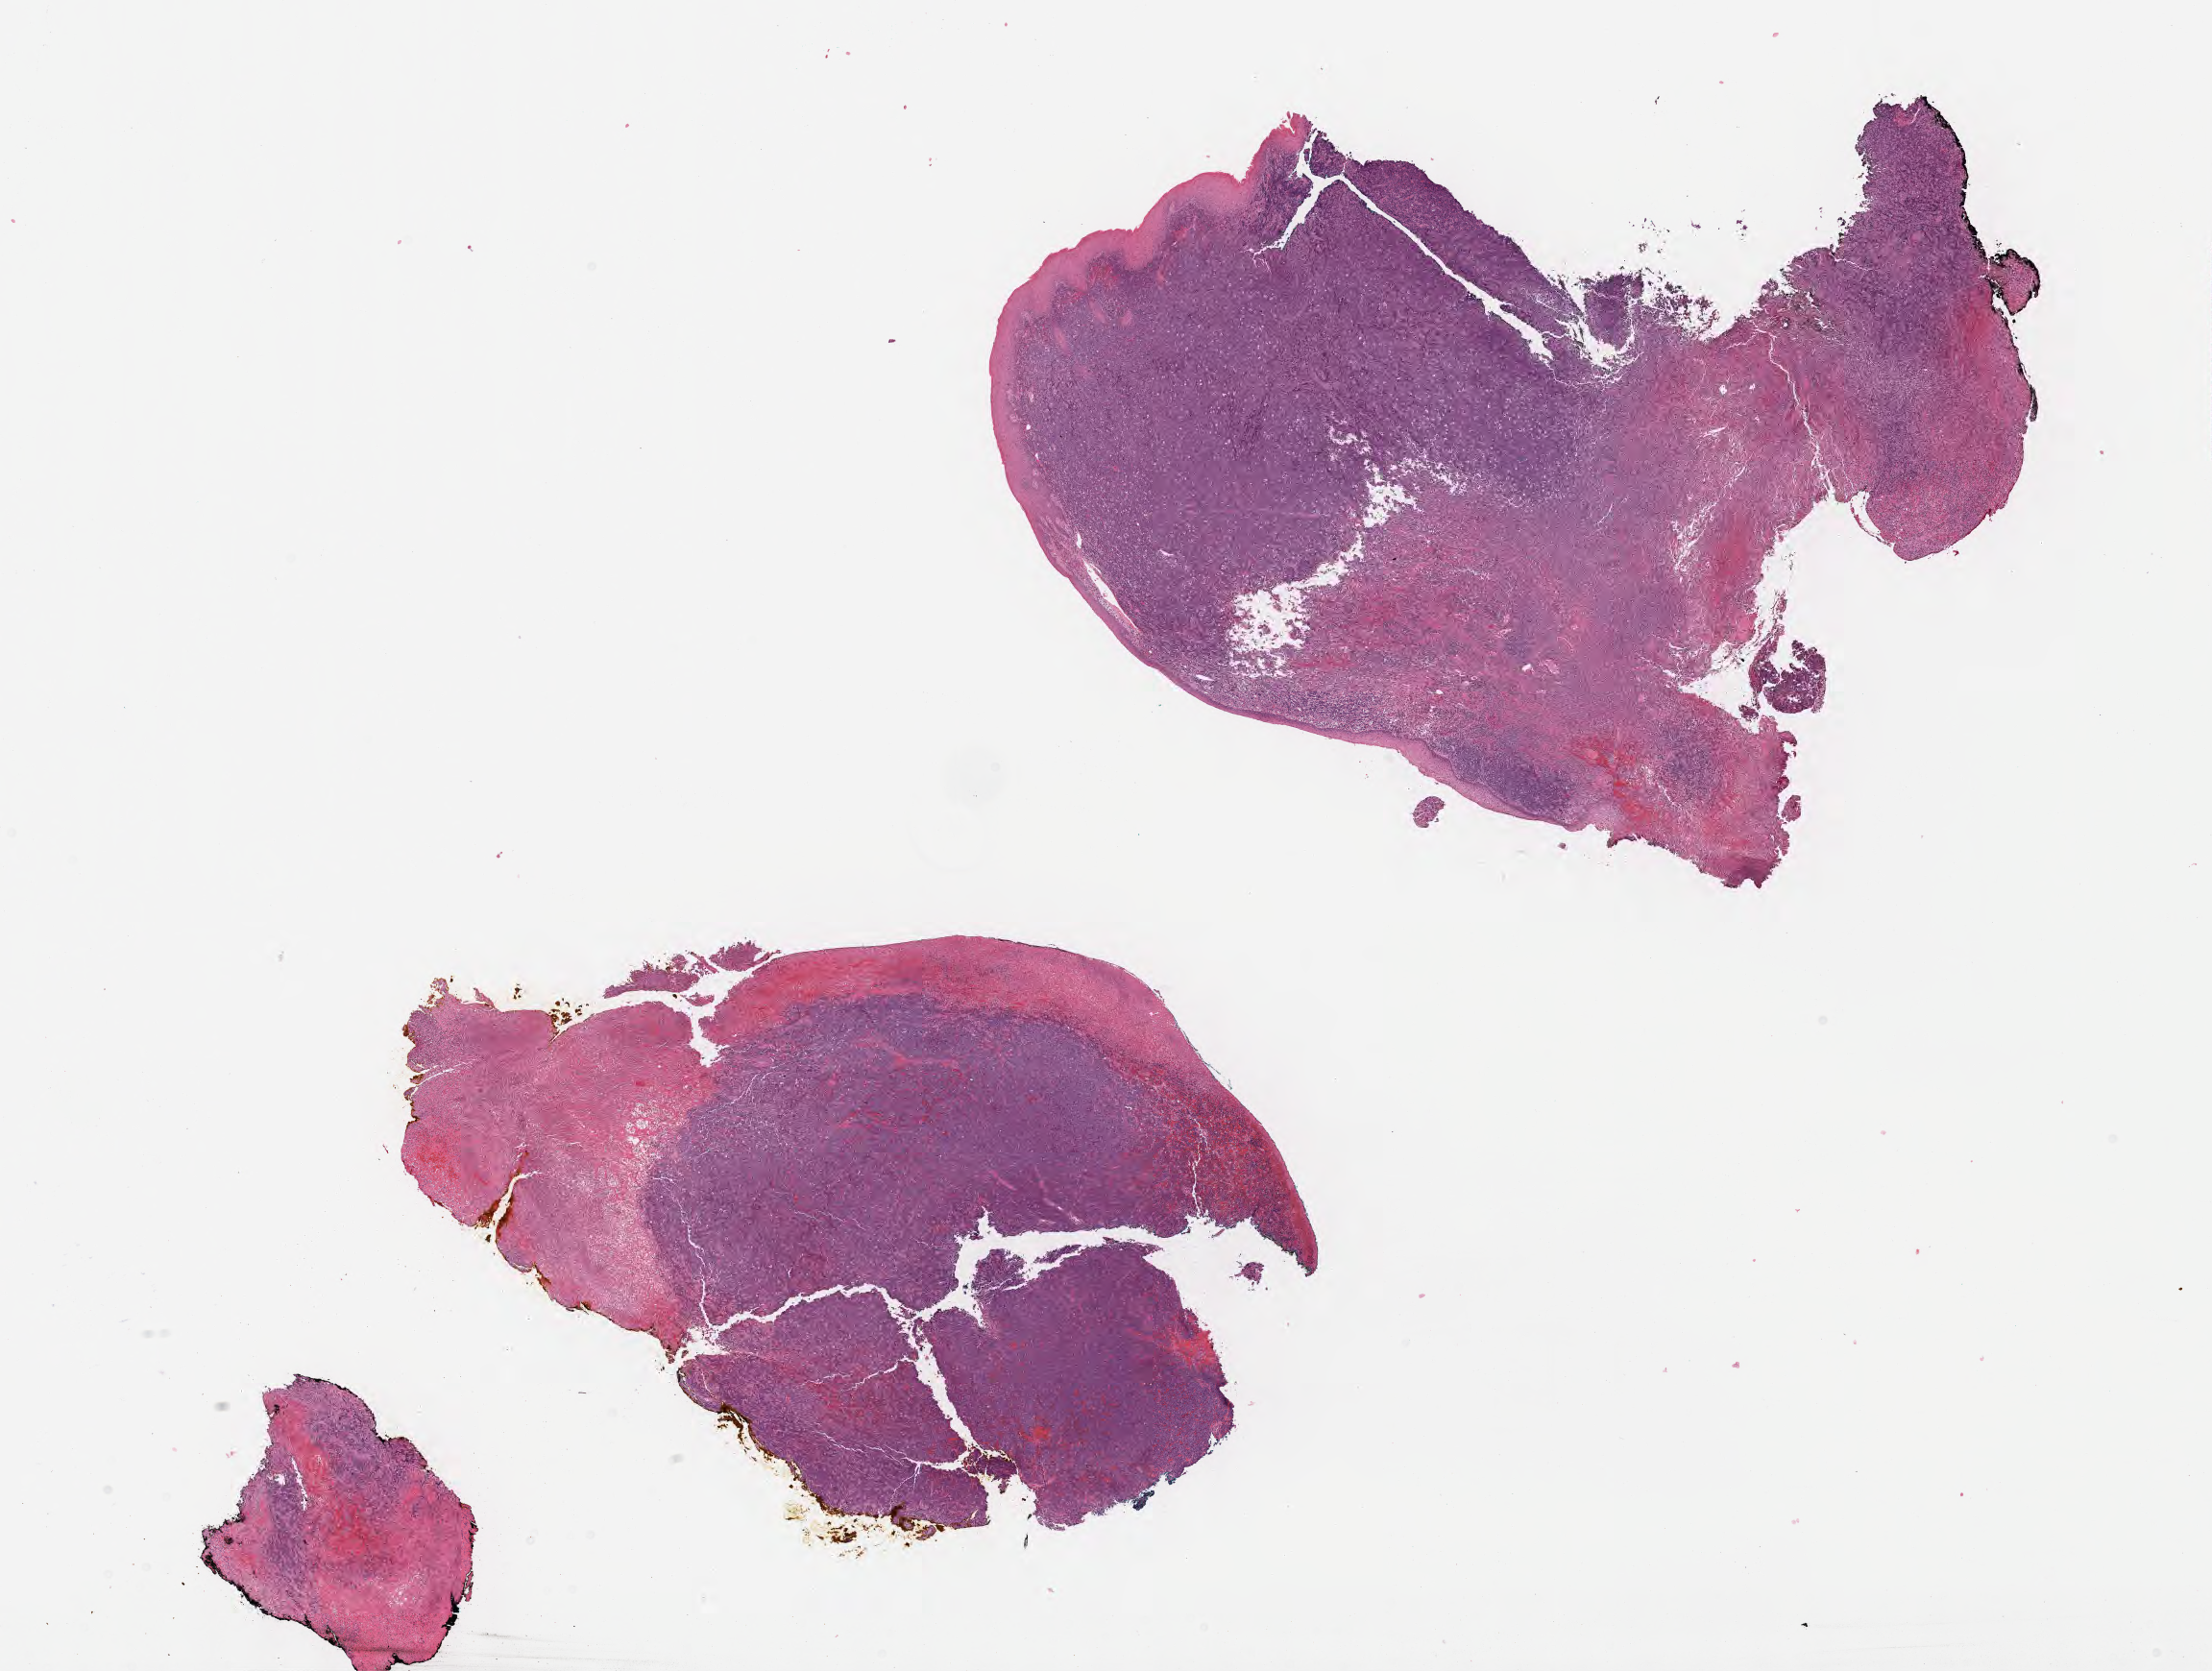
Haematoxylin and eosin whole-slide image — whole scanned area (about 18.6 x 14.1 mm) shown as a low-resolution overview. Specimen: tumor tissue. Patient male; aged 49.
Histologic diagnosis: Diffuse large B-cell lymphoma, NOS.